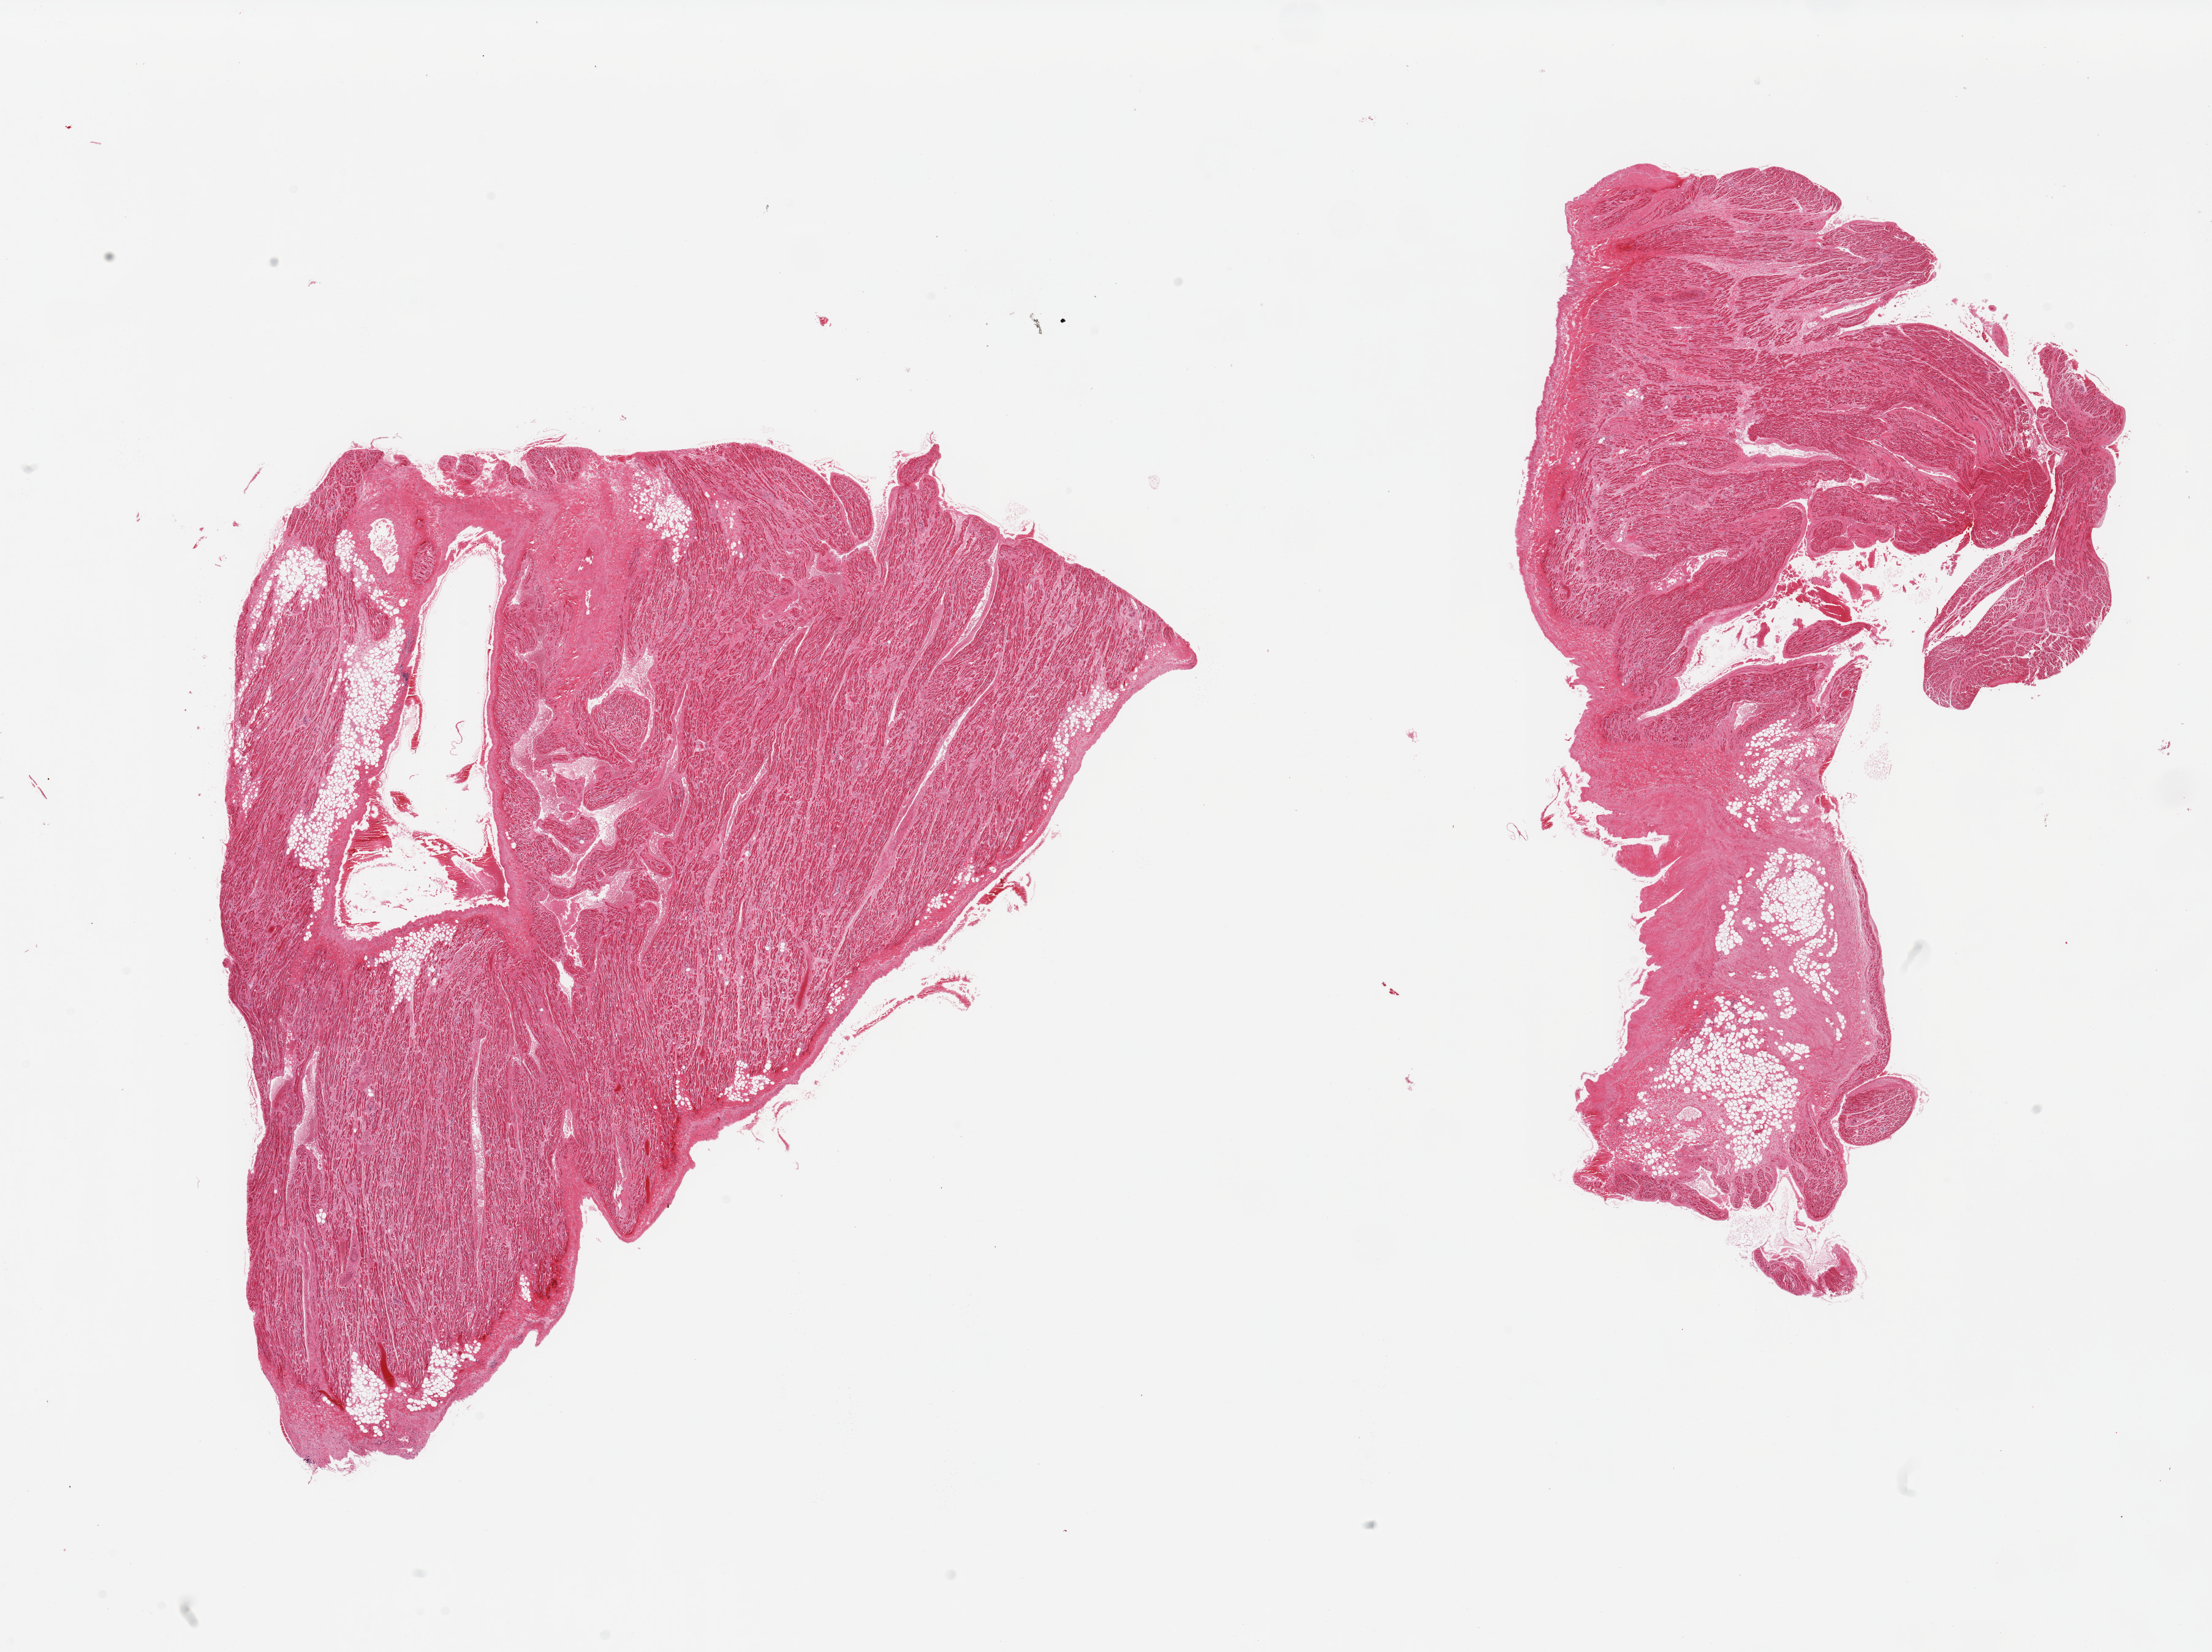
Whole-slide image, H&E stain — a low-resolution overview of the entire scanned area, about 28.5 x 21.3 mm, PAXgene-fixed paraffin-embedded (PFPE) section, section of auricular appendage (target tissue), donor tissue sample.
Reviewer comment on this tissue sample: 2 pieces; 30% fibromuscular tissue on 1 piece; 5% internal fat on other piece.